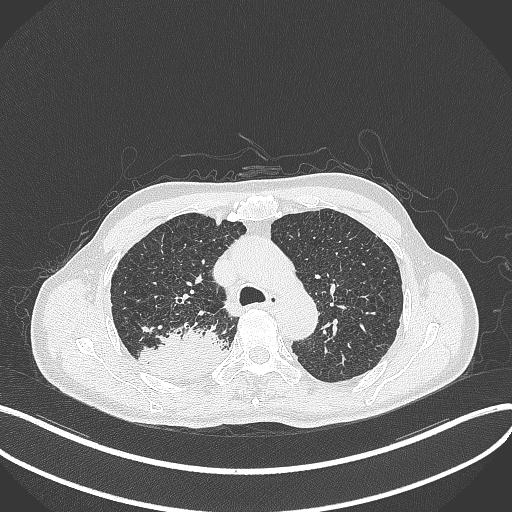
Chest CT, one axial slice. Slice 324 of 428 in the series (ordered by position). Lung window (W 1500 / L -600 HU). 1 mm slice thickness. 512 × 512 image matrix. Patient: male, 79 years. From the clinical record (not read from this slice): clinical TNM (as recorded): T3 N0 M0.
Structures marked on this image (rectangle marked by the reading radiologist):
- lung tumour (recorded histology: adenocarcinoma): box from (x=135, y=322) to (x=233, y=381) px